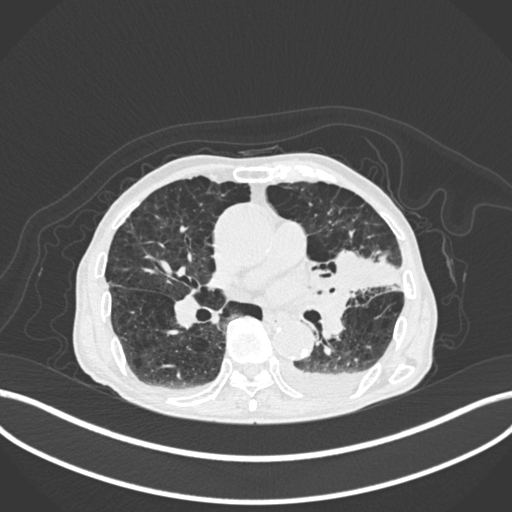
Chest CT, one axial slice; position 111 of 400 along the scan axis; reconstruction kernel B30f; 120 kVp; lung window (W 1500 / L -600 HU); 512 × 512 image matrix. Patient: male, 90 years or older. Case-level facts recorded for this patient, not image findings: clinical TNM (as recorded): T2b N1 M0.
Annotated regions visible in this slice (bounding box drawn by a radiologist):
- lung tumour (recorded histology: squamous cell carcinoma): bounding box <330,243,398,295> (left, top, right, bottom; pixels)